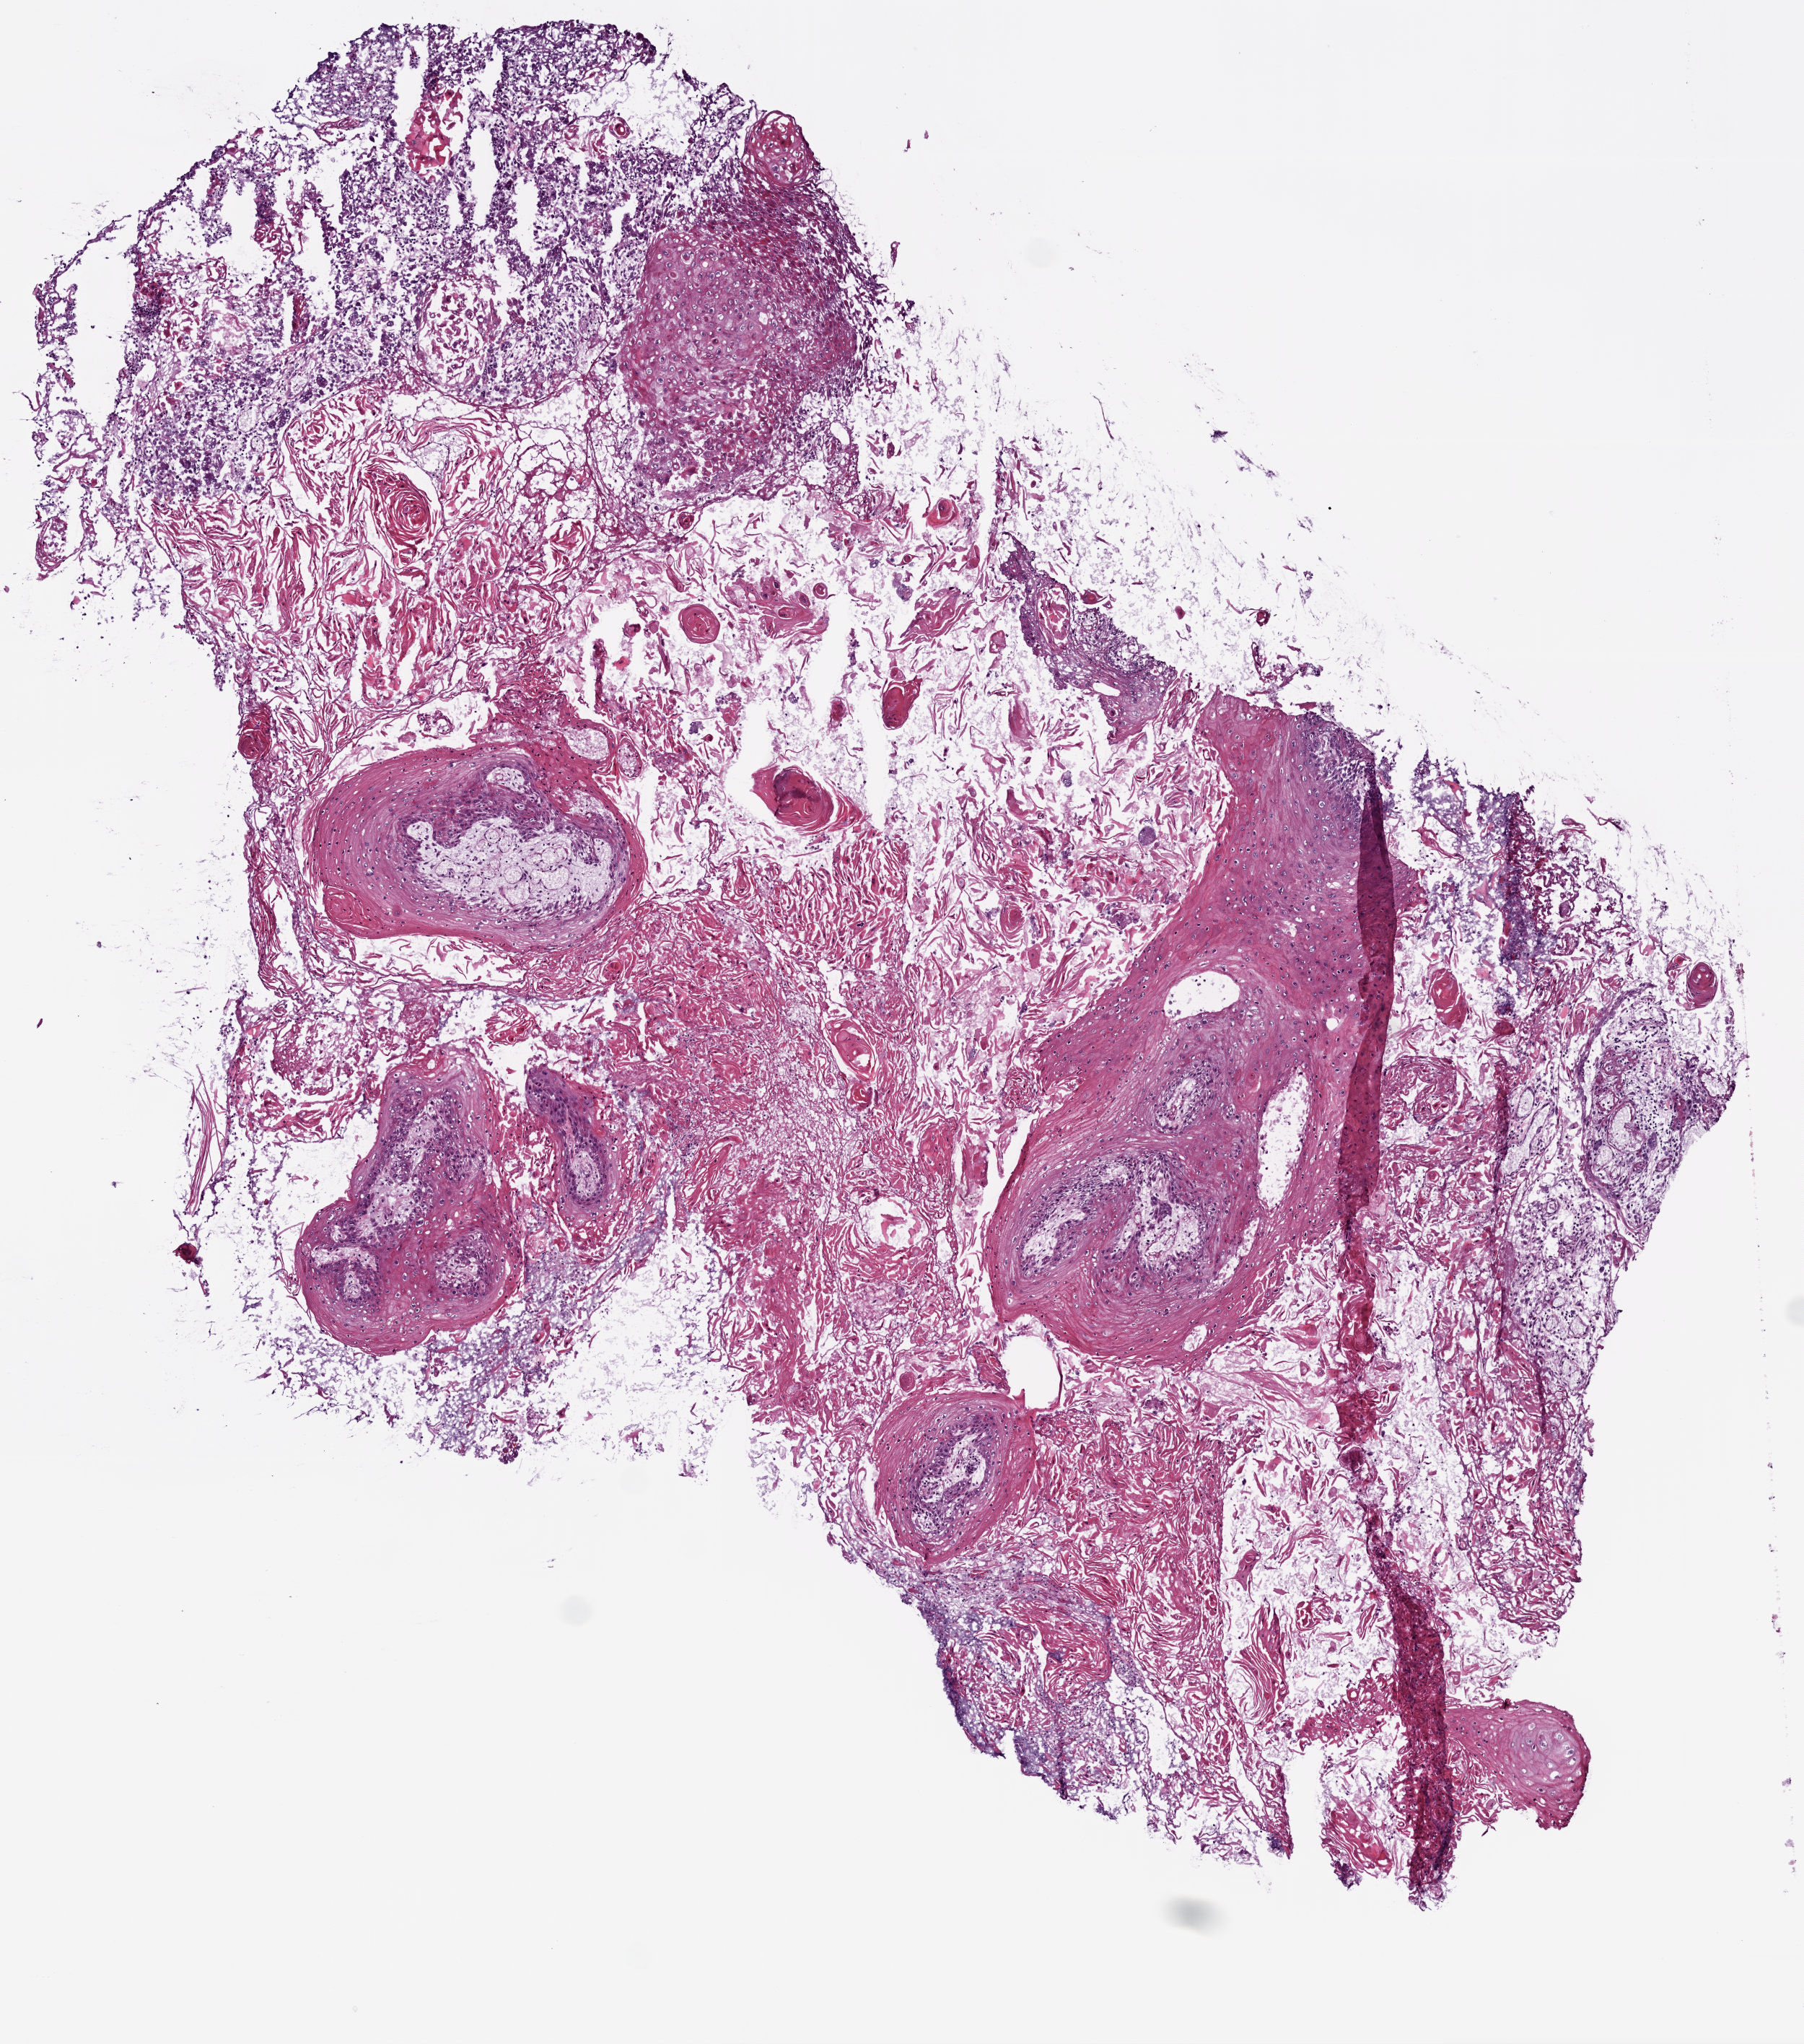
Digitized H&E tissue section (whole slide), shown as a low-resolution overview of the whole scanned area (about 5.0 x 5.7 mm); frozen section; head and neck, primary tumour sample. Female patient; age at initial diagnosis 41 years. Histologic grade: G2 (moderately differentiated). Slide review estimates, as recorded: tumour cells 48%, tumour nuclei 75%, normal cells 0%, stromal cells 50%, necrosis 2%.
* AJCC pathologic stage: III
* lymph nodes positive (case pathology): 1 of 34 examined
* diagnosis: Squamous cell carcinoma, NOS (overlapping lesion of lip, oral cavity and pharynx)